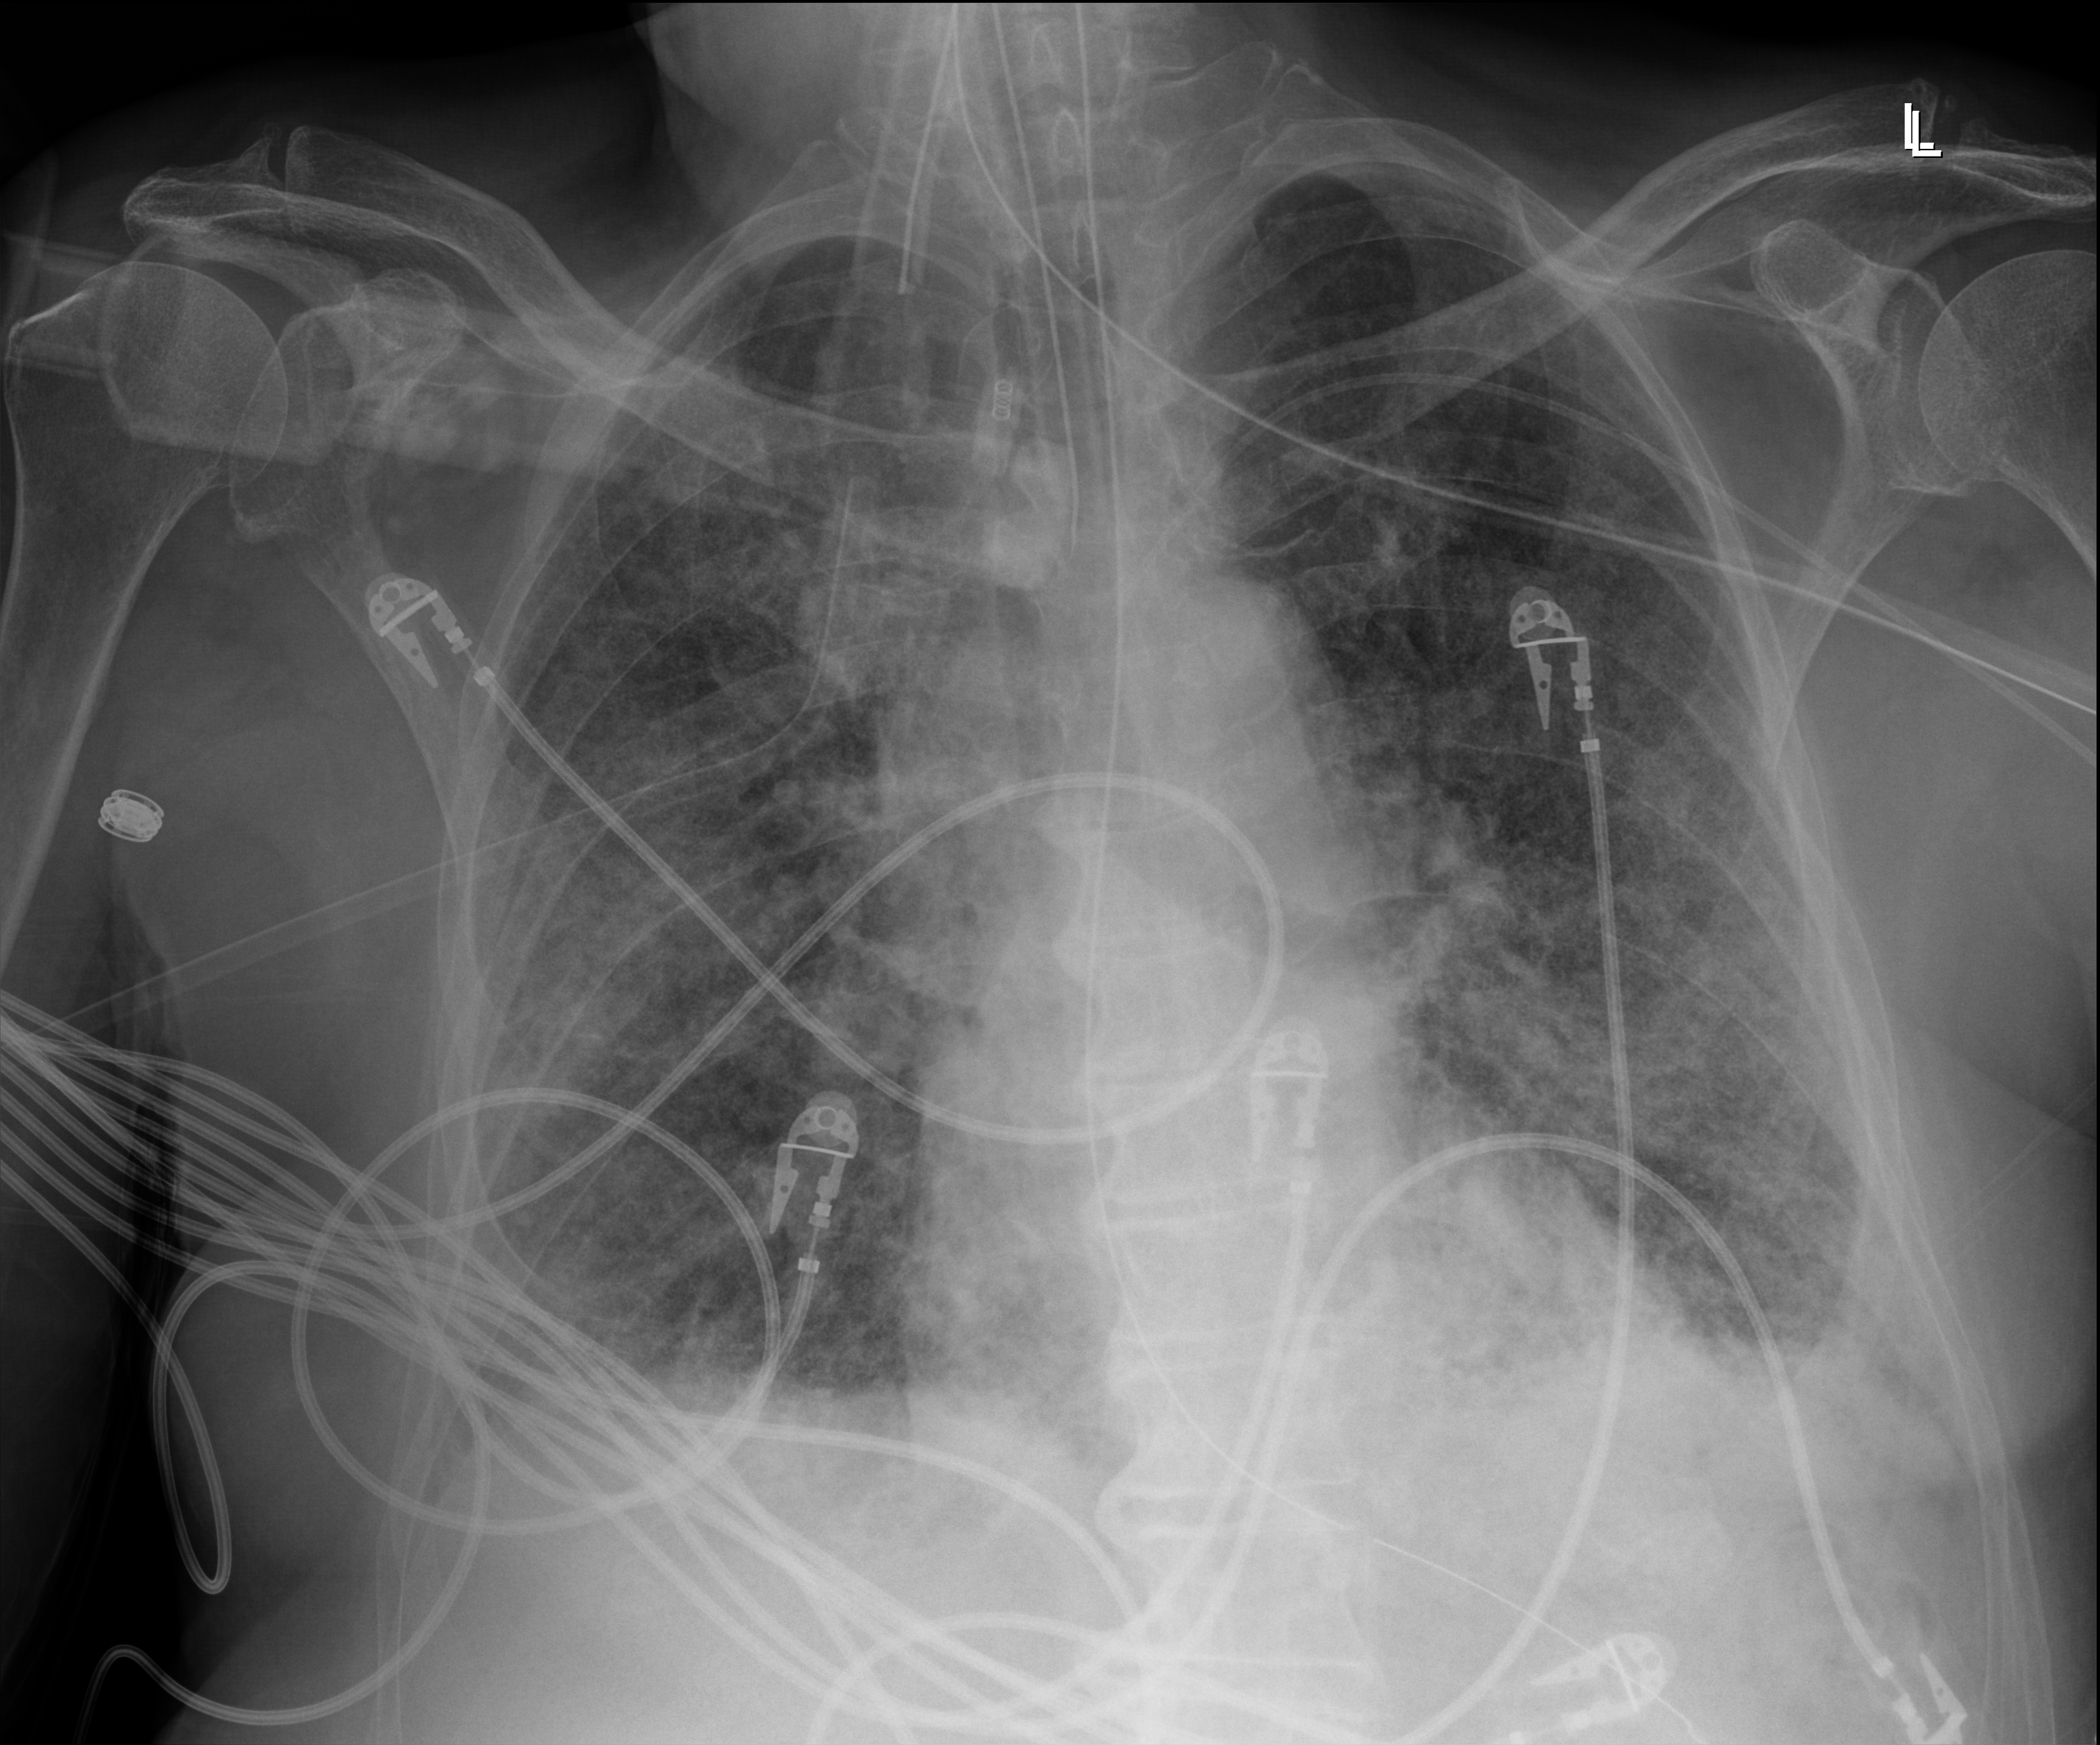
Bedside chest radiograph (digital radiography), anteroposterior (AP) projection. Male patient hospitalised with COVID-19, age 75–90 years.
Admission-level facts for this patient (not findings on this image; timing relative to this image not recorded): other chronic lung disease (admission record): no; mechanically ventilated during this hospital stay: yes; admitted to intensive care during this hospital stay: yes.